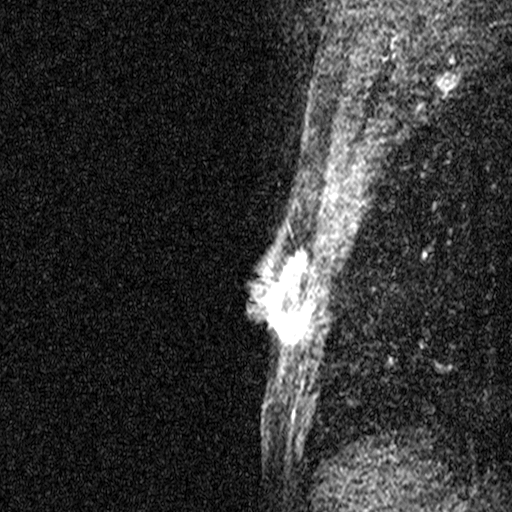
Breast MRI (dynamic contrast-enhanced), one sagittal slice; position 31 of 44 along the scan axis; dynamic contrast-enhanced study with each time point stored as its own series, time point 2 of 3 at this slice position (early post-contrast, ordered by acquisition time); 1.5 T; TE 4.5 ms, TR 11 ms; 512 × 512 image matrix, field of view 200 × 200 mm. Female patient, age 45 years. Case-level facts recorded for this patient, not image findings: setting: breast cancer imaged before/during neoadjuvant chemotherapy; receptor status: HR-positive, HER2-negative.
Outlined on this slice (semi-automatic segmentation, software-assisted and operator-edited):
- analysis volume of interest (the breast-tissue region the enhancement analysis was run in; not a lesion): bounding box [x1, y1, x2, y2] px = [256, 218, 318, 359]
- tumour enhancement mask (voxels above the 90 % enhancement threshold inside the analysis volume of interest): [268, 243, 311, 332]